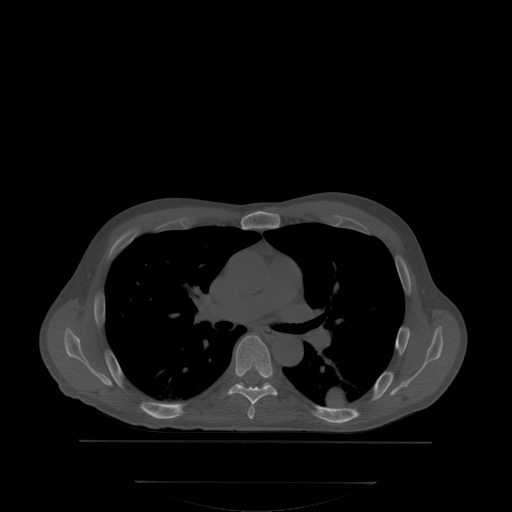
CT including the spine, one axial slice. Slice 237 of 350 in the series (ordered by position). Bone window (W 1800 / L 400 HU). 512 × 512 image matrix. Male patient, age 58 years. Case-level facts recorded for this patient, not image findings: primary cancer: prostate; vertebrae with lytic lesions (as recorded): L1.
Outlined on this slice (semi-automatically segmented with operator editing):
- T6 vertebra: bounding box <230,335,276,417> (left, top, right, bottom; pixels)
- T7 vertebra: <238,382,272,387>